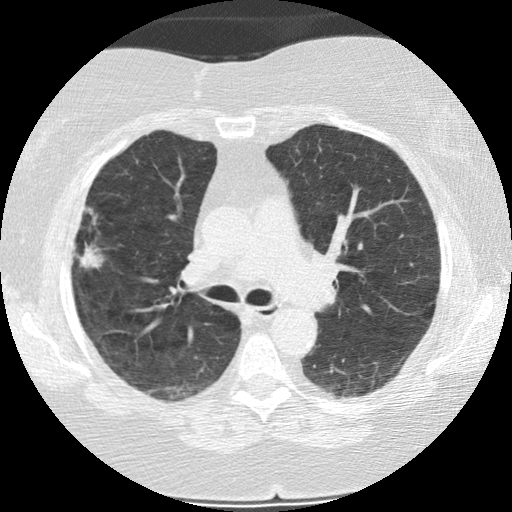
Axial slice from a low-dose chest CT screening exam. Baseline annual screen. Lung window (W 1500 / L -600 HU). 2.5 mm slice thickness. Standard (soft-tissue) reconstruction kernel (STANDARD). 120 kVp. Slice 73 of 187 in the series. 512 × 512 image matrix. Female, age 73 years at enrolment. Former smoker at enrolment.
- Expert reader's lesion annotation, box from (x=59, y=211) to (x=111, y=276) px.
- Screening reader's record for this exam (one nodule recorded; not confirmed to be the boxed lesion): non-calcified nodule or mass ≥4 mm, right upper lobe, 21 × 14 mm, poorly defined margins, soft tissue attenuation.